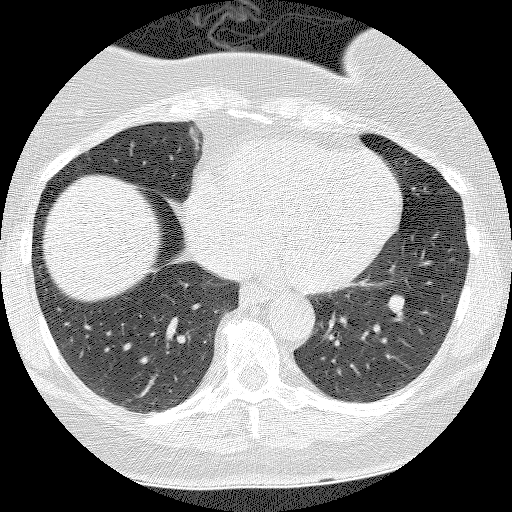
Low-dose screening chest CT, axial slice. Baseline annual screen. Lung window (W 1500 / L -600 HU). 2.5 mm slice thickness. Lung (sharp) reconstruction kernel (BONE). Slice 91 of 135 in the series. Female, age 55 years at enrolment. Former smoker at enrolment.
Expert reader's lesion annotation, box from (x=372, y=286) to (x=420, y=328) px. The screening reader recorded 3 non-calcified nodules or masses ≥4 mm on this exam (left lower lobe, right lower lobe, right lower lobe); which of them this box marks is not recorded. Official screen result: positive, change unspecified: nodule(s) >= 4 mm or enlarging nodule(s), mass(es), or other non-specific abnormalities suspicious for lung cancer. Participant outcome: lung cancer diagnosed 1026 days after this screen — carcinoid tumor, NOS, left lower lobe, carcinoid, stage not assessed, 10 mm at pathology.